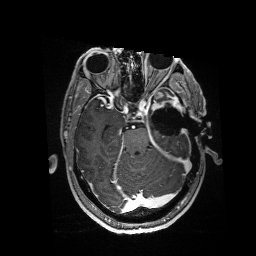
Brain MRI from a brain-tumour surgery series, one axial slice; position 106 of 176 along the scan axis; T1-weighted post-contrast; 1 mm slice thickness; 256 × 256 image matrix, field of view 256 × 256 mm. From the clinical record (not read from this slice): histopathology: Glioblastoma; WHO grade: 4; IDH mutation: no; tumour location: Left Anterior/Superior Temporal.
Annotated regions visible in this slice (manually delineated by an expert):
- residual tumour: box from (x=152, y=92) to (x=185, y=116) px